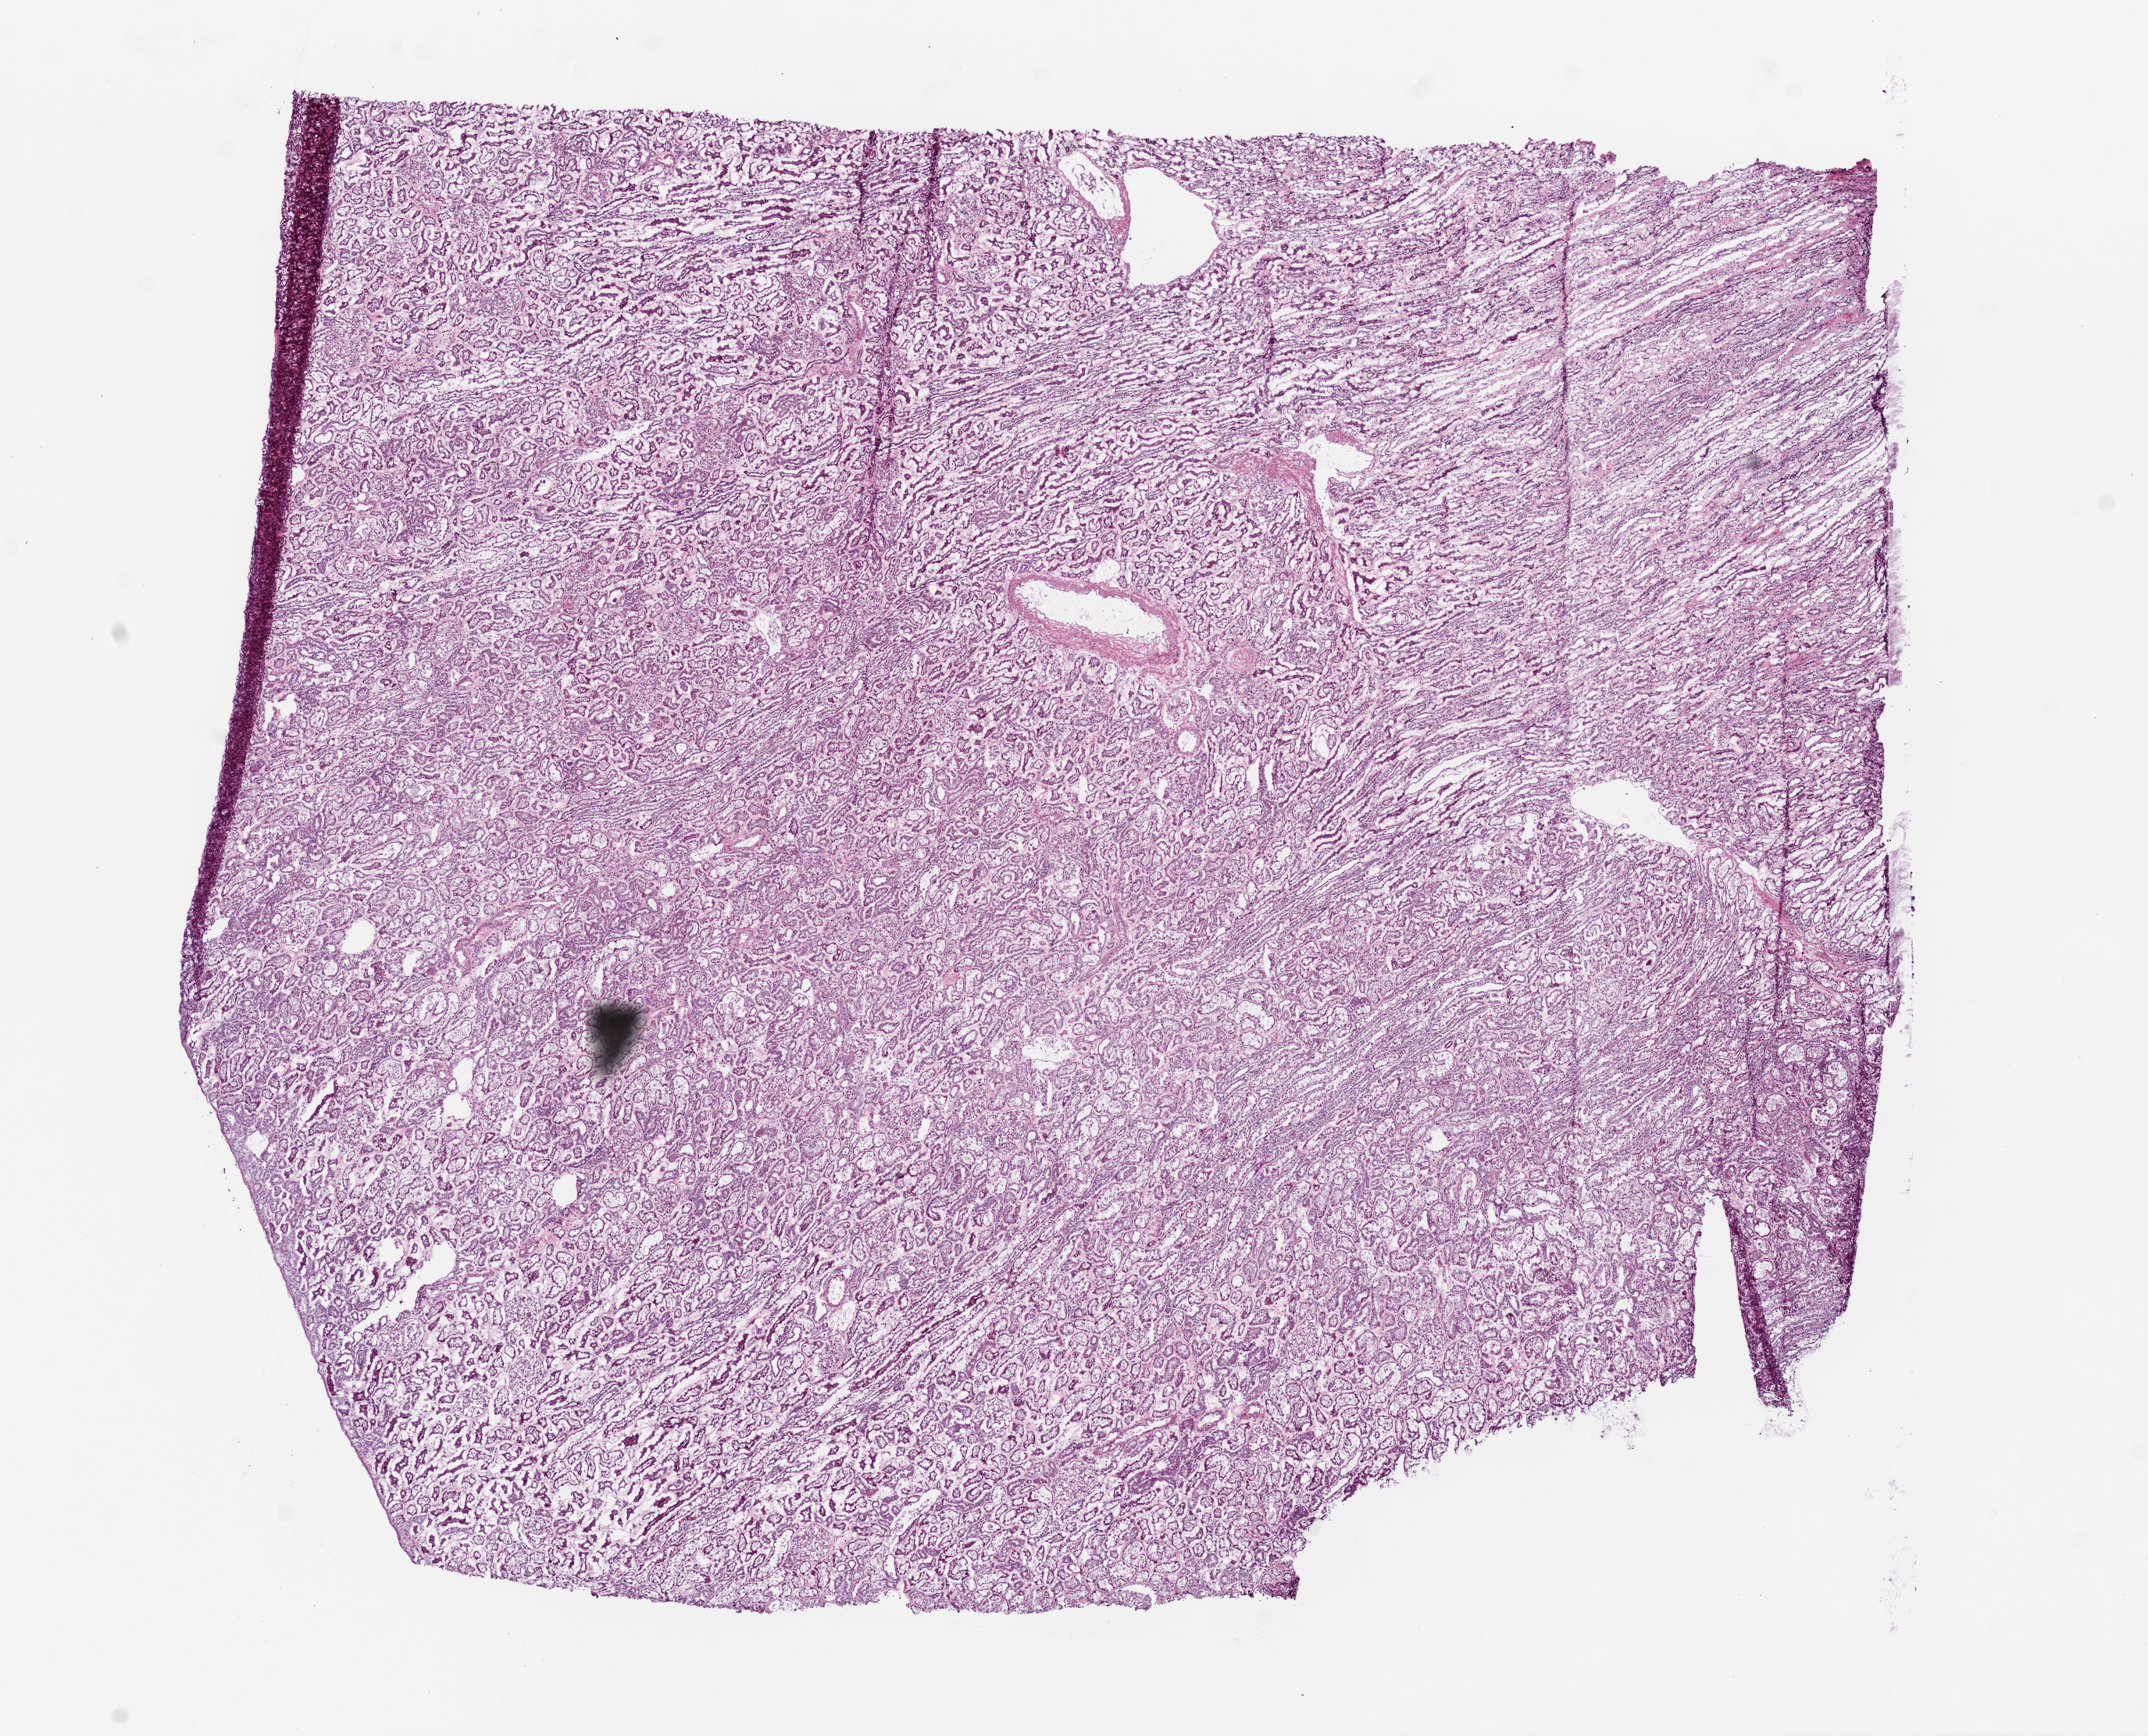
Whole-slide histology image, H&E-stained — whole scanned area (about 11.0 x 8.9 mm, from a 20x scan) shown as a low-resolution overview, frozen section from the top of the tissue portion, kidney, solid tissue normal (non-tumour tissue) sample. Male, age 44 years at initial diagnosis.
• this section: solid tissue normal (non-tumour) sample from the same patient
• patient diagnosis: Clear cell adenocarcinoma, NOS